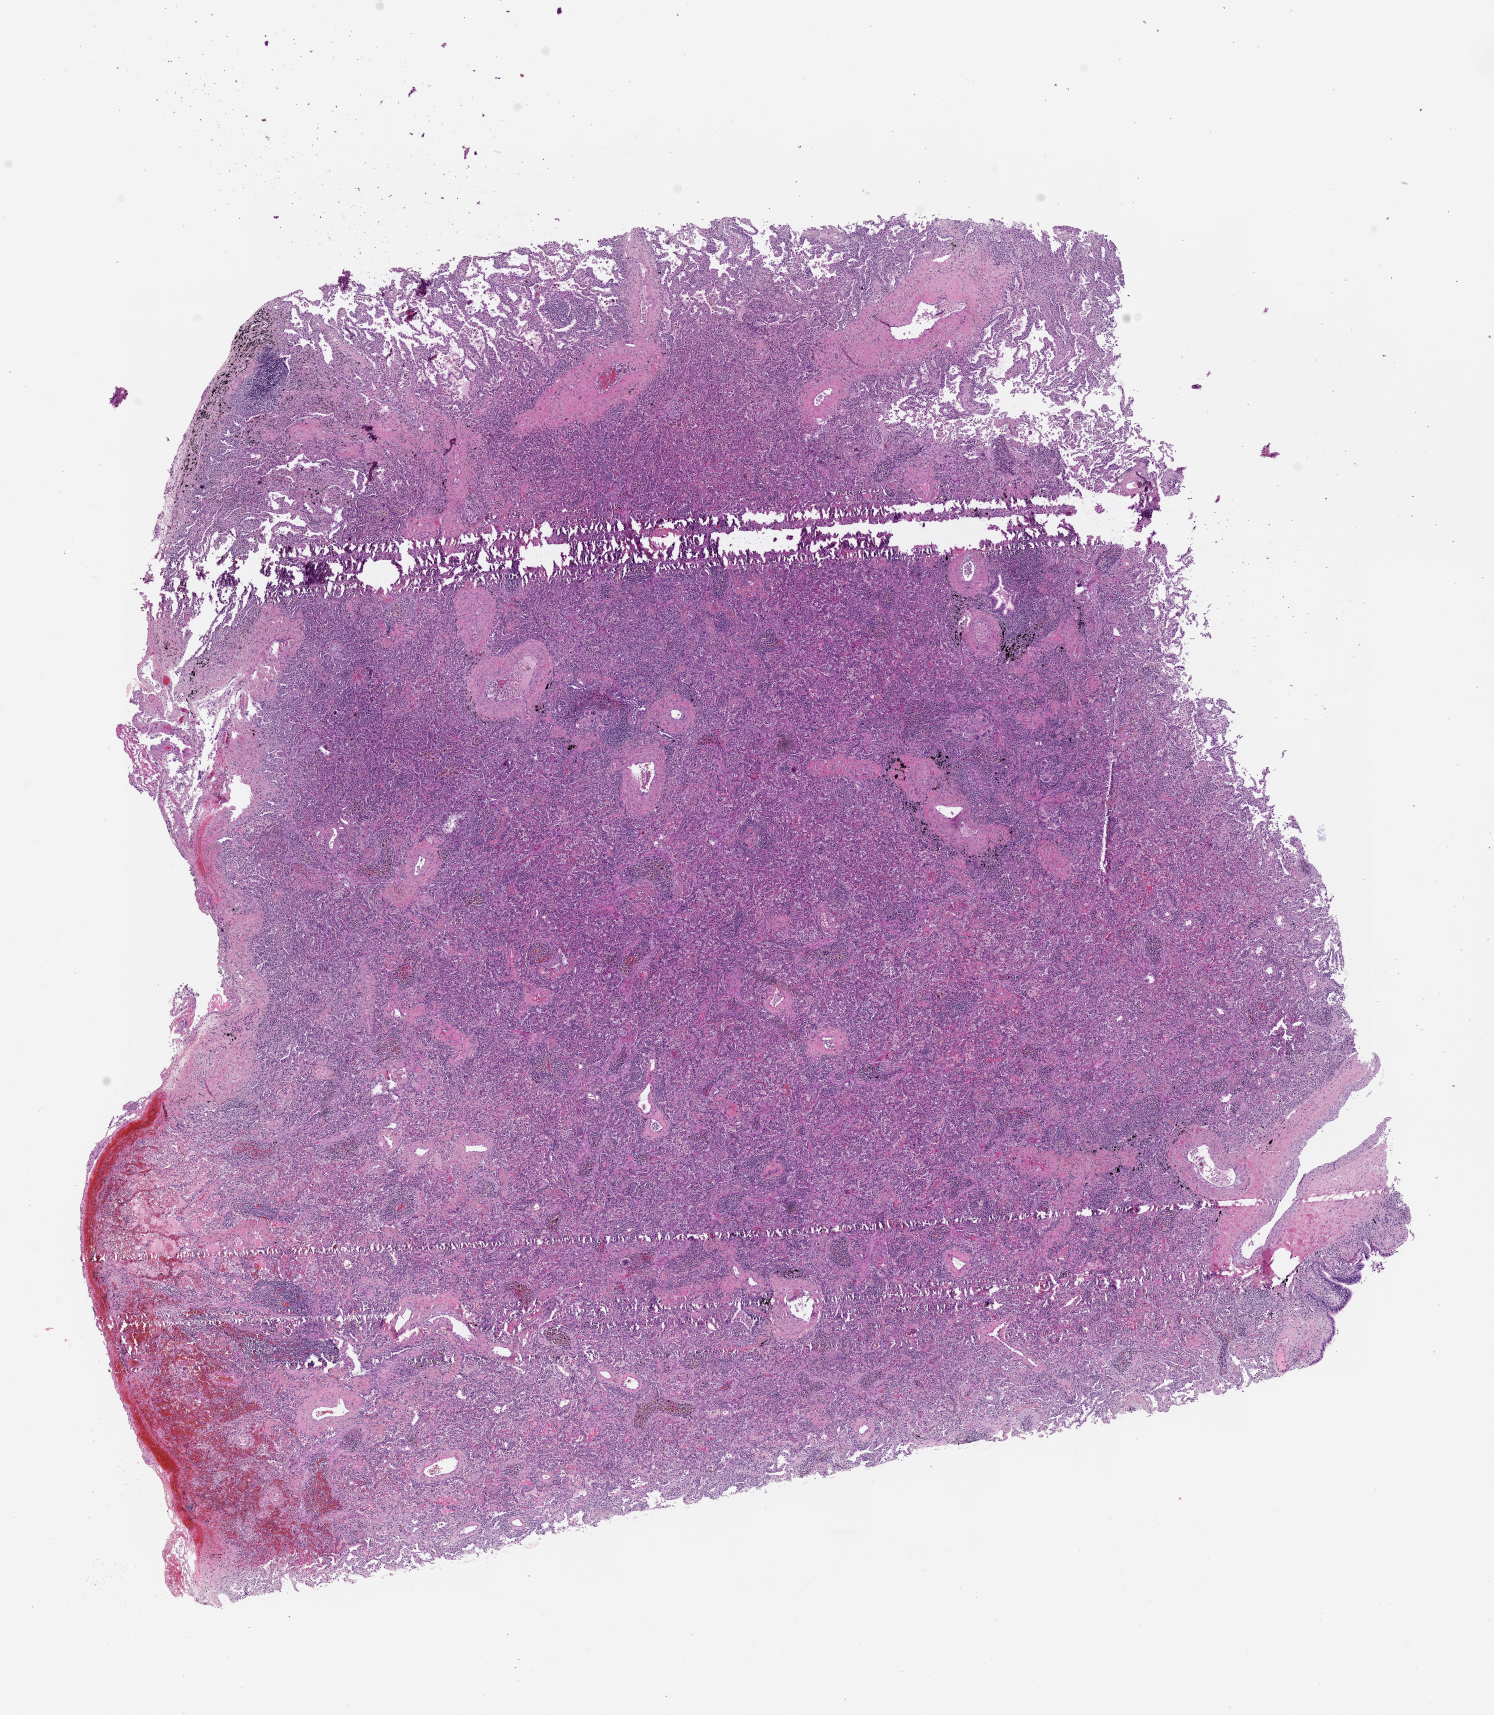
H&E whole-slide image, whole scanned area (about 12.0 x 13.8 mm) shown as a low-resolution overview, lung, normal (non-tumour) tissue. Patient: male, age 64 years.
This section: normal (non-tumour) tissue from the same patient. Patient diagnosis (cohort enrolment): squamous cell carcinoma (lung).